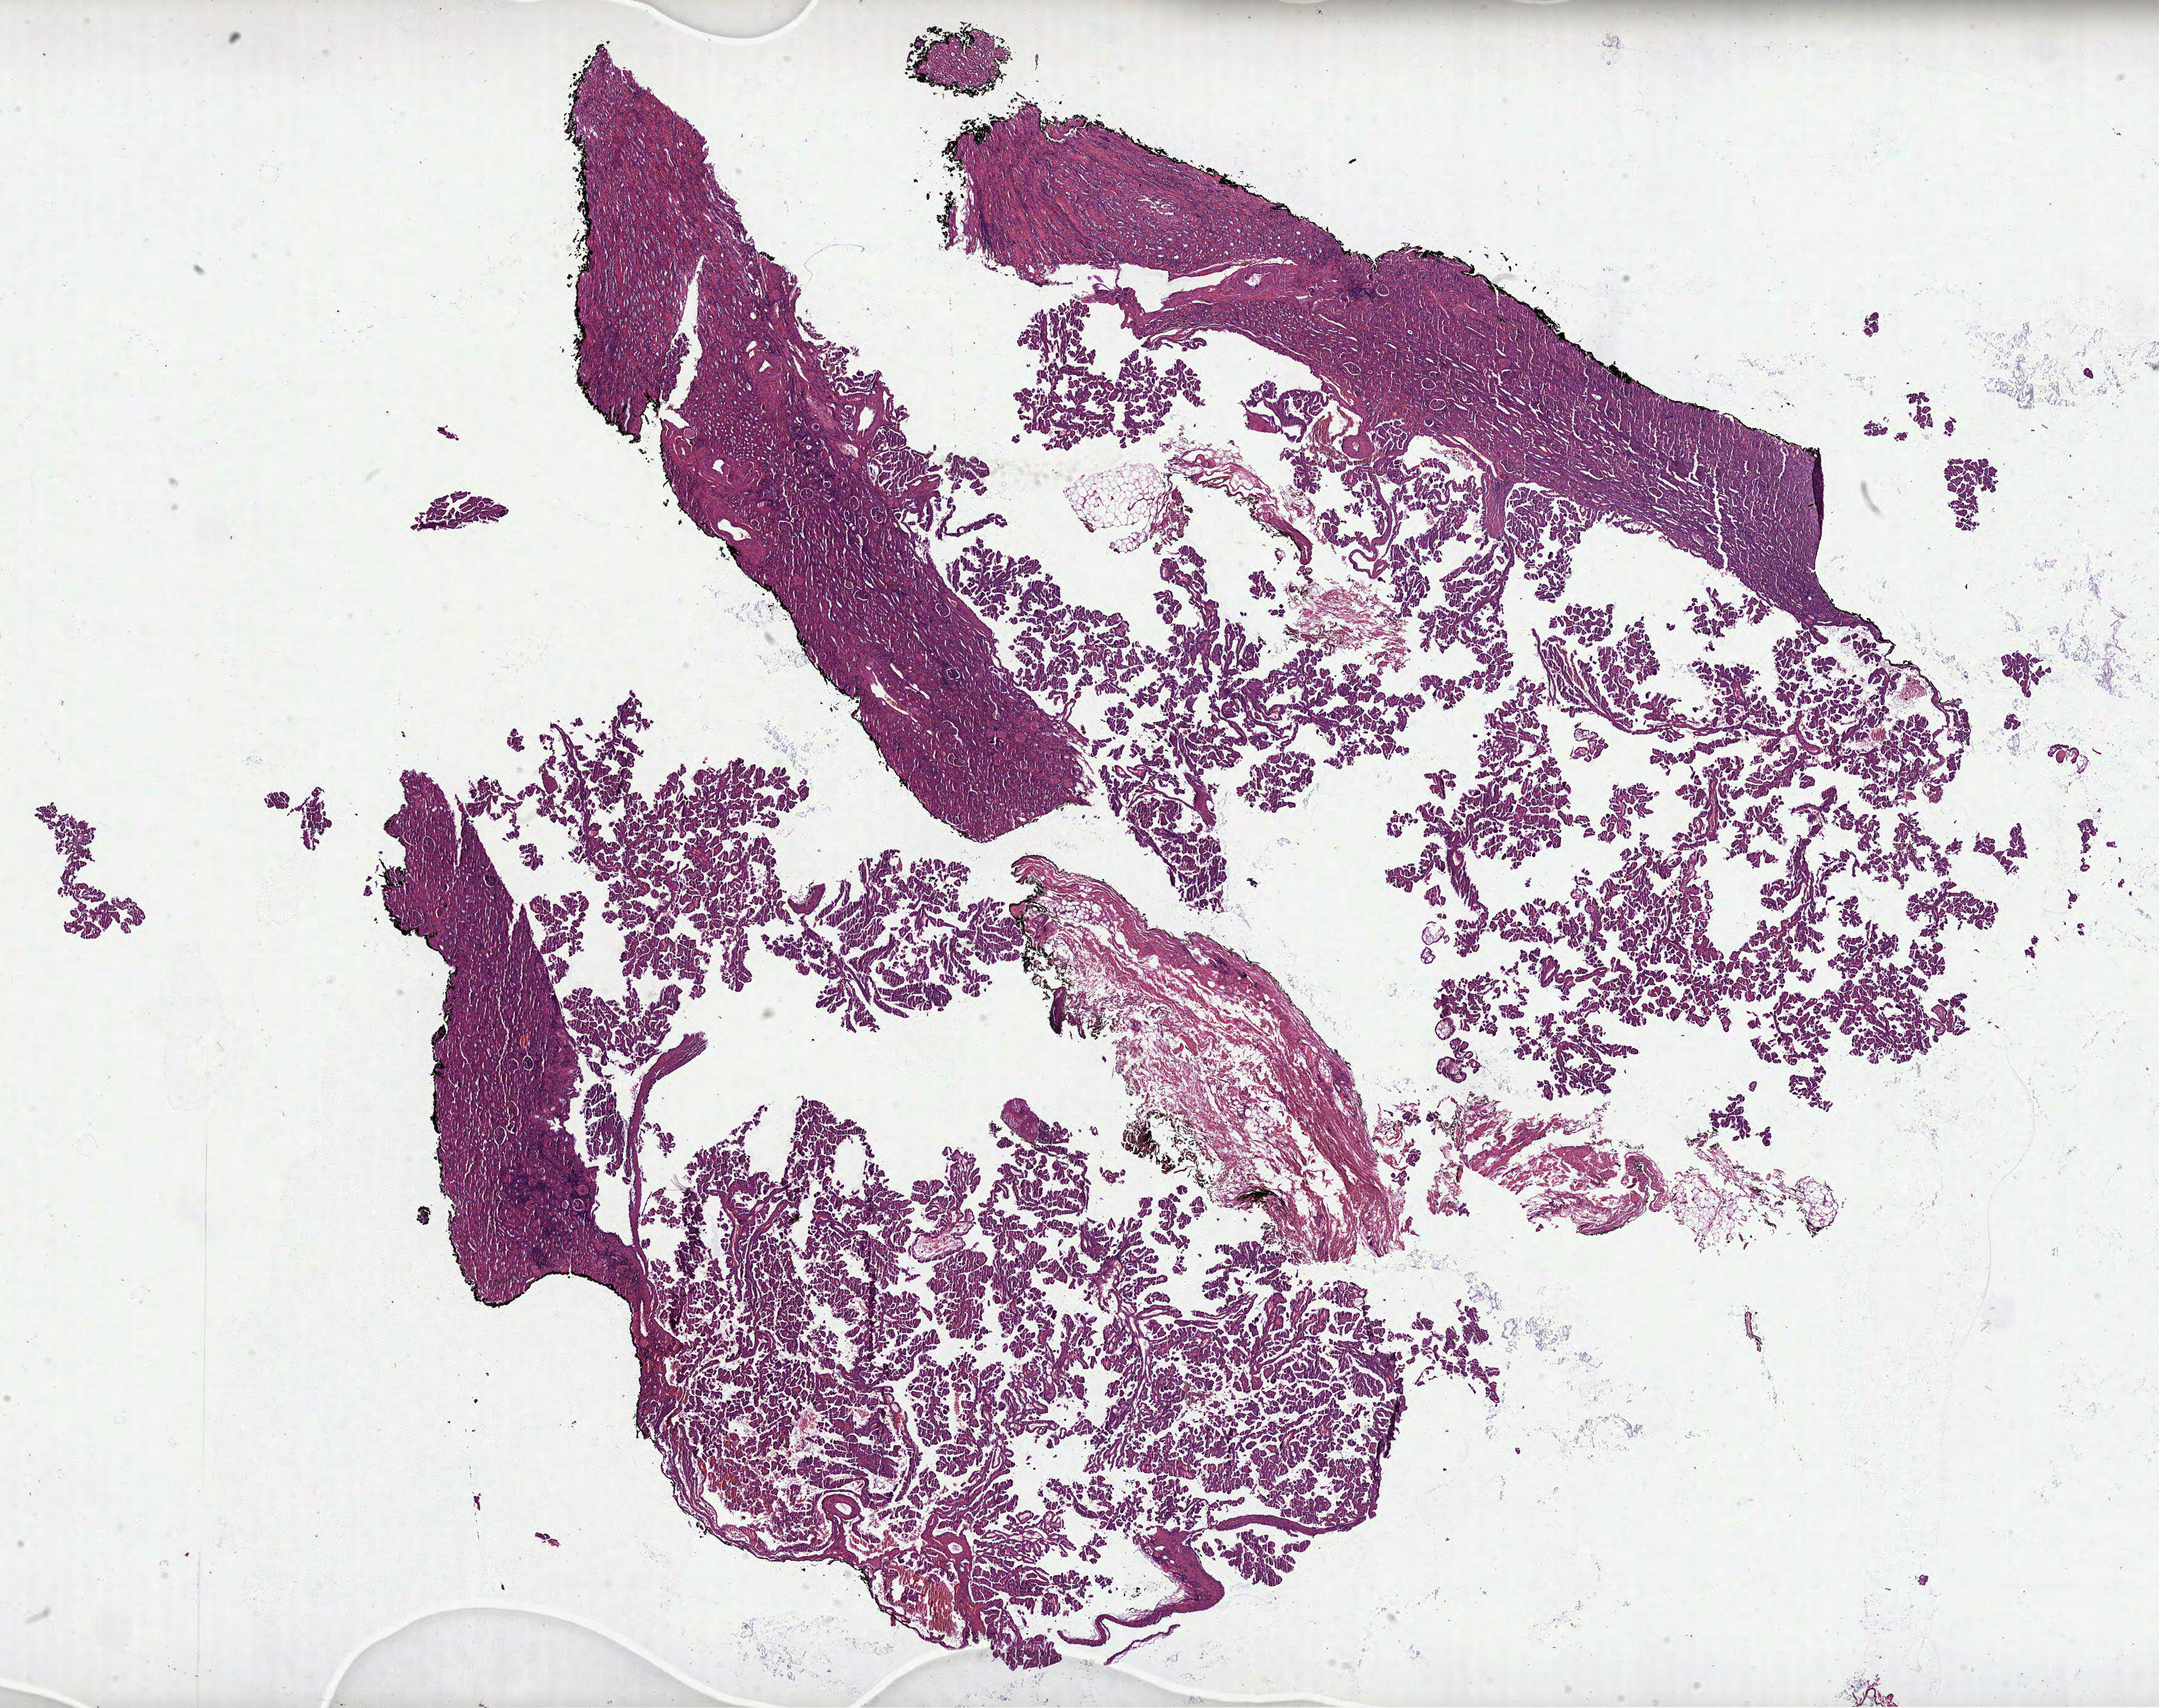
Whole-slide histology image, H&E-stained — shown as a low-resolution overview of the whole scanned area (about 28.0 x 22.2 mm), FFPE section, sample: primary tumour, kidney. Male, age 60 years at initial diagnosis.
* laterality: left
* AJCC pathologic stage: I
* TNM: T1 NX MX
* histologic diagnosis: Papillary adenocarcinoma, NOS